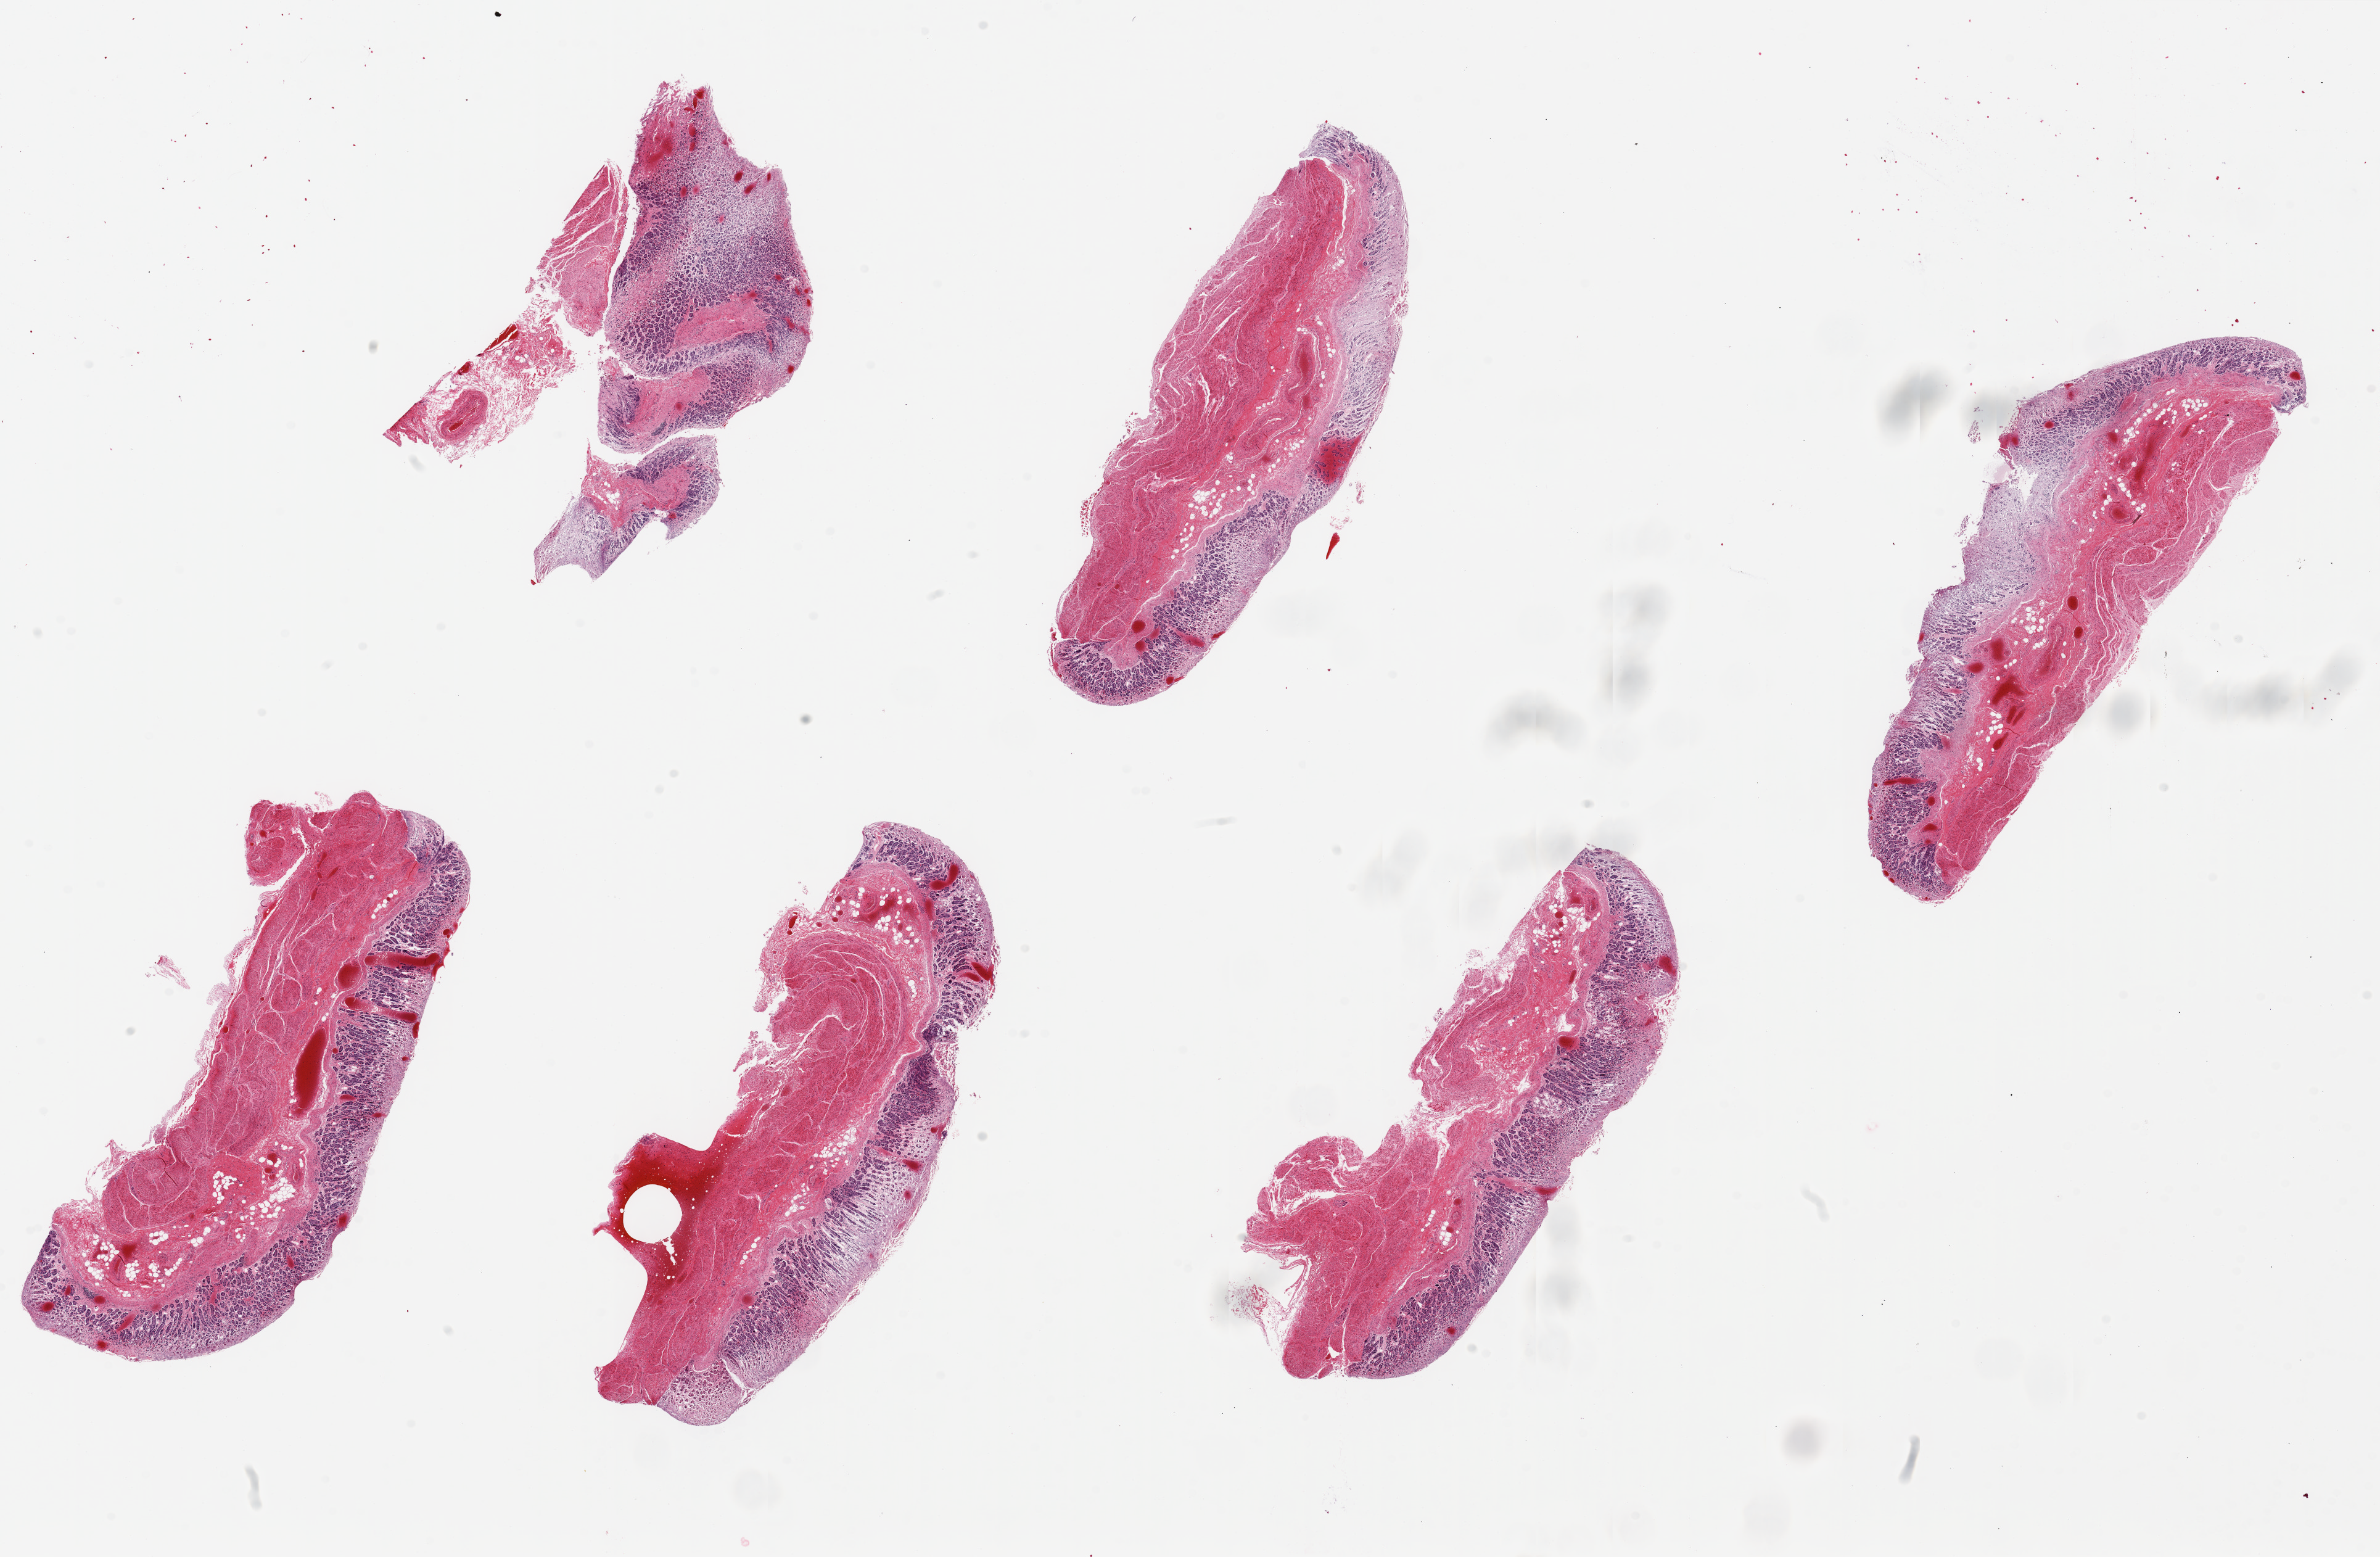
H&E whole-slide image, brightfield — low-resolution overview of the scanned area, about 30.5 x 20.0 mm (slide scanned at 20x), PAXgene-fixed paraffin-embedded (PFPE) section, target tissue: stomach, tissue donor sample. Male donor.
Pathologist's review note for this sample: 6 pieces ~8x3mm; mucosa is ~20-30% thickness but moderately-severely autolyzed.